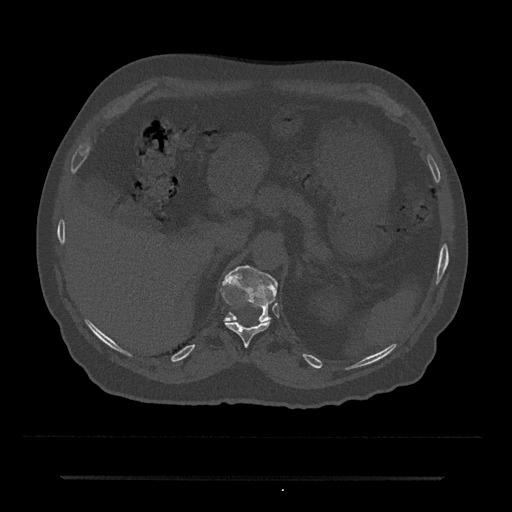
CT including the spine, one axial slice; slice 162 of 797 in the series (ordered by position); reconstruction kernel Br40s/3; 120 kVp; bone window (W 1800 / L 400 HU); 0.5 mm slice thickness; 512 × 512 image matrix, field of view 437 × 437 mm. Patient: male, 69 years. From the clinical record (not read from this slice): primary cancer: prostate.
Structures marked on this image (semi-automatic segmentation, software-assisted and operator-edited):
- T11 vertebra: box from (x=225, y=321) to (x=270, y=347) px
- T12 vertebra: (x=225, y=265)–(x=278, y=322)